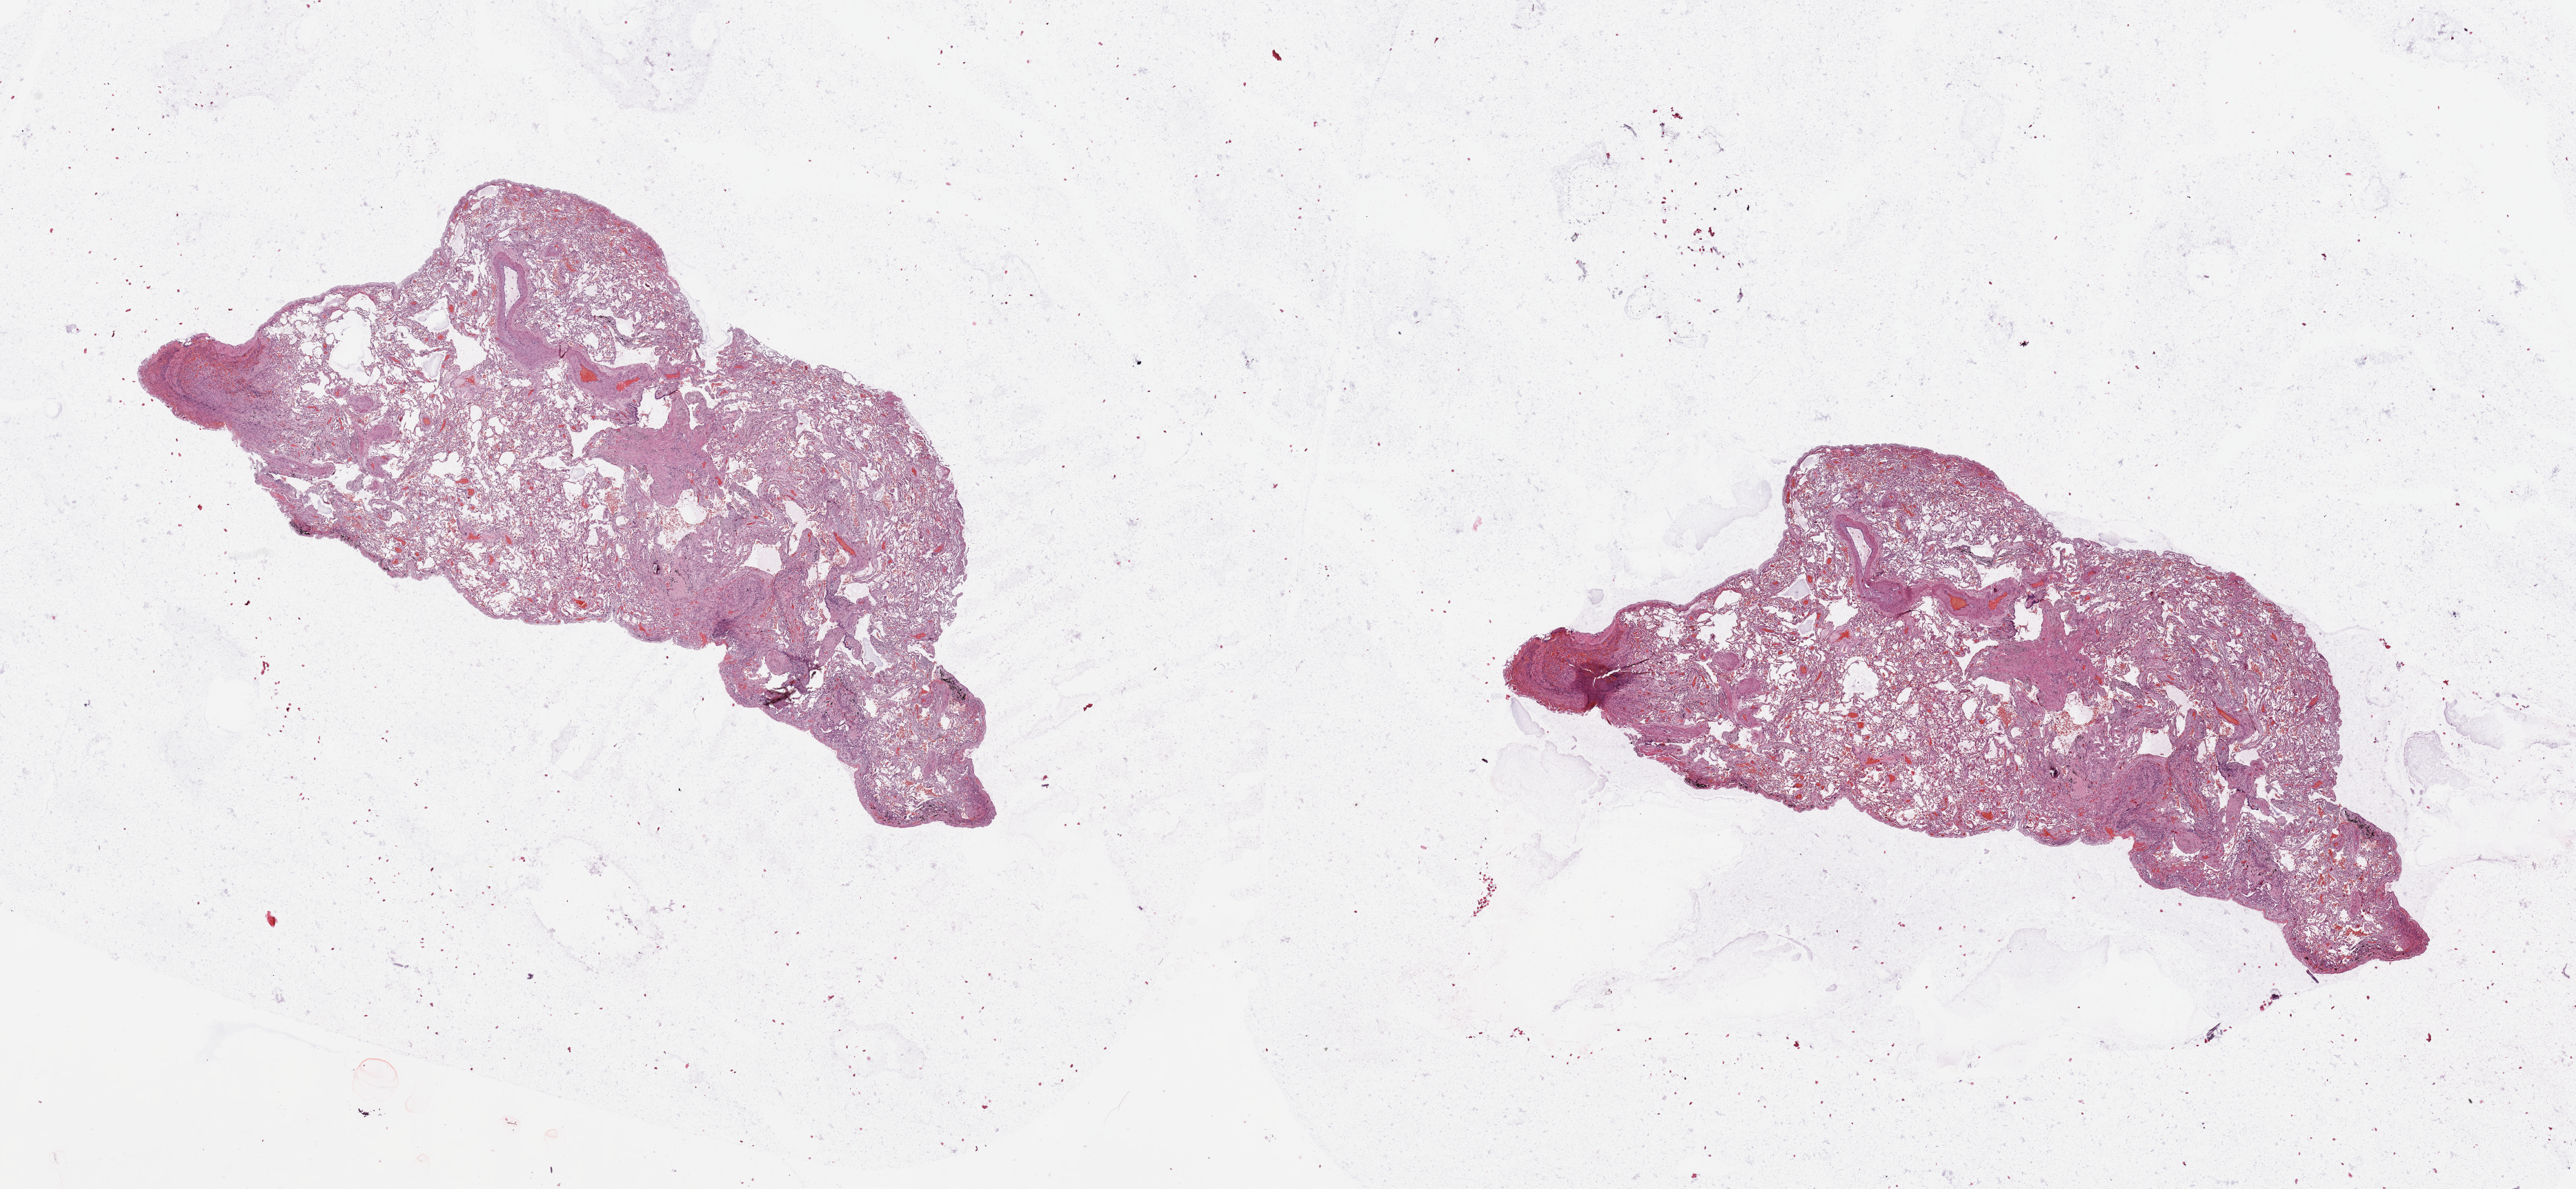
Digitized H&E-stained tissue section (whole slide), low-resolution overview of the scanned area, about 29.5 x 13.6 mm (slide scanned at 20x); normal (non-tumour) tissue sample, sampled site: lung. Male, 72 y/o.
• this section: normal (non-tumour) tissue from the same patient
• patient diagnosis: Squamous cell carcinoma, NOS